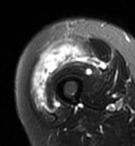
MRI of an extremity soft-tissue mass, one axial slice; position 21 of 95 along the scan axis; T2-weighted fat-saturated; MR volume resampled by the dataset authors to the PET/CT grid (not the native acquisition matrix); 3.27 mm slice thickness; 135 × 146 image matrix. Female patient. Case-level facts recorded for this patient, not image findings: histological type: pleiomorphic undifferentiated sarcoma; grade: high; site of the primary tumour: right quadricep.
Outlined on this slice (expert contour drawn on MRI and transferred to this co-registered scan by the dataset authors):
- gross tumour volume including surrounding oedema: bounding box (x1, y1, x2, y2) in pixels: (32, 43, 90, 108)